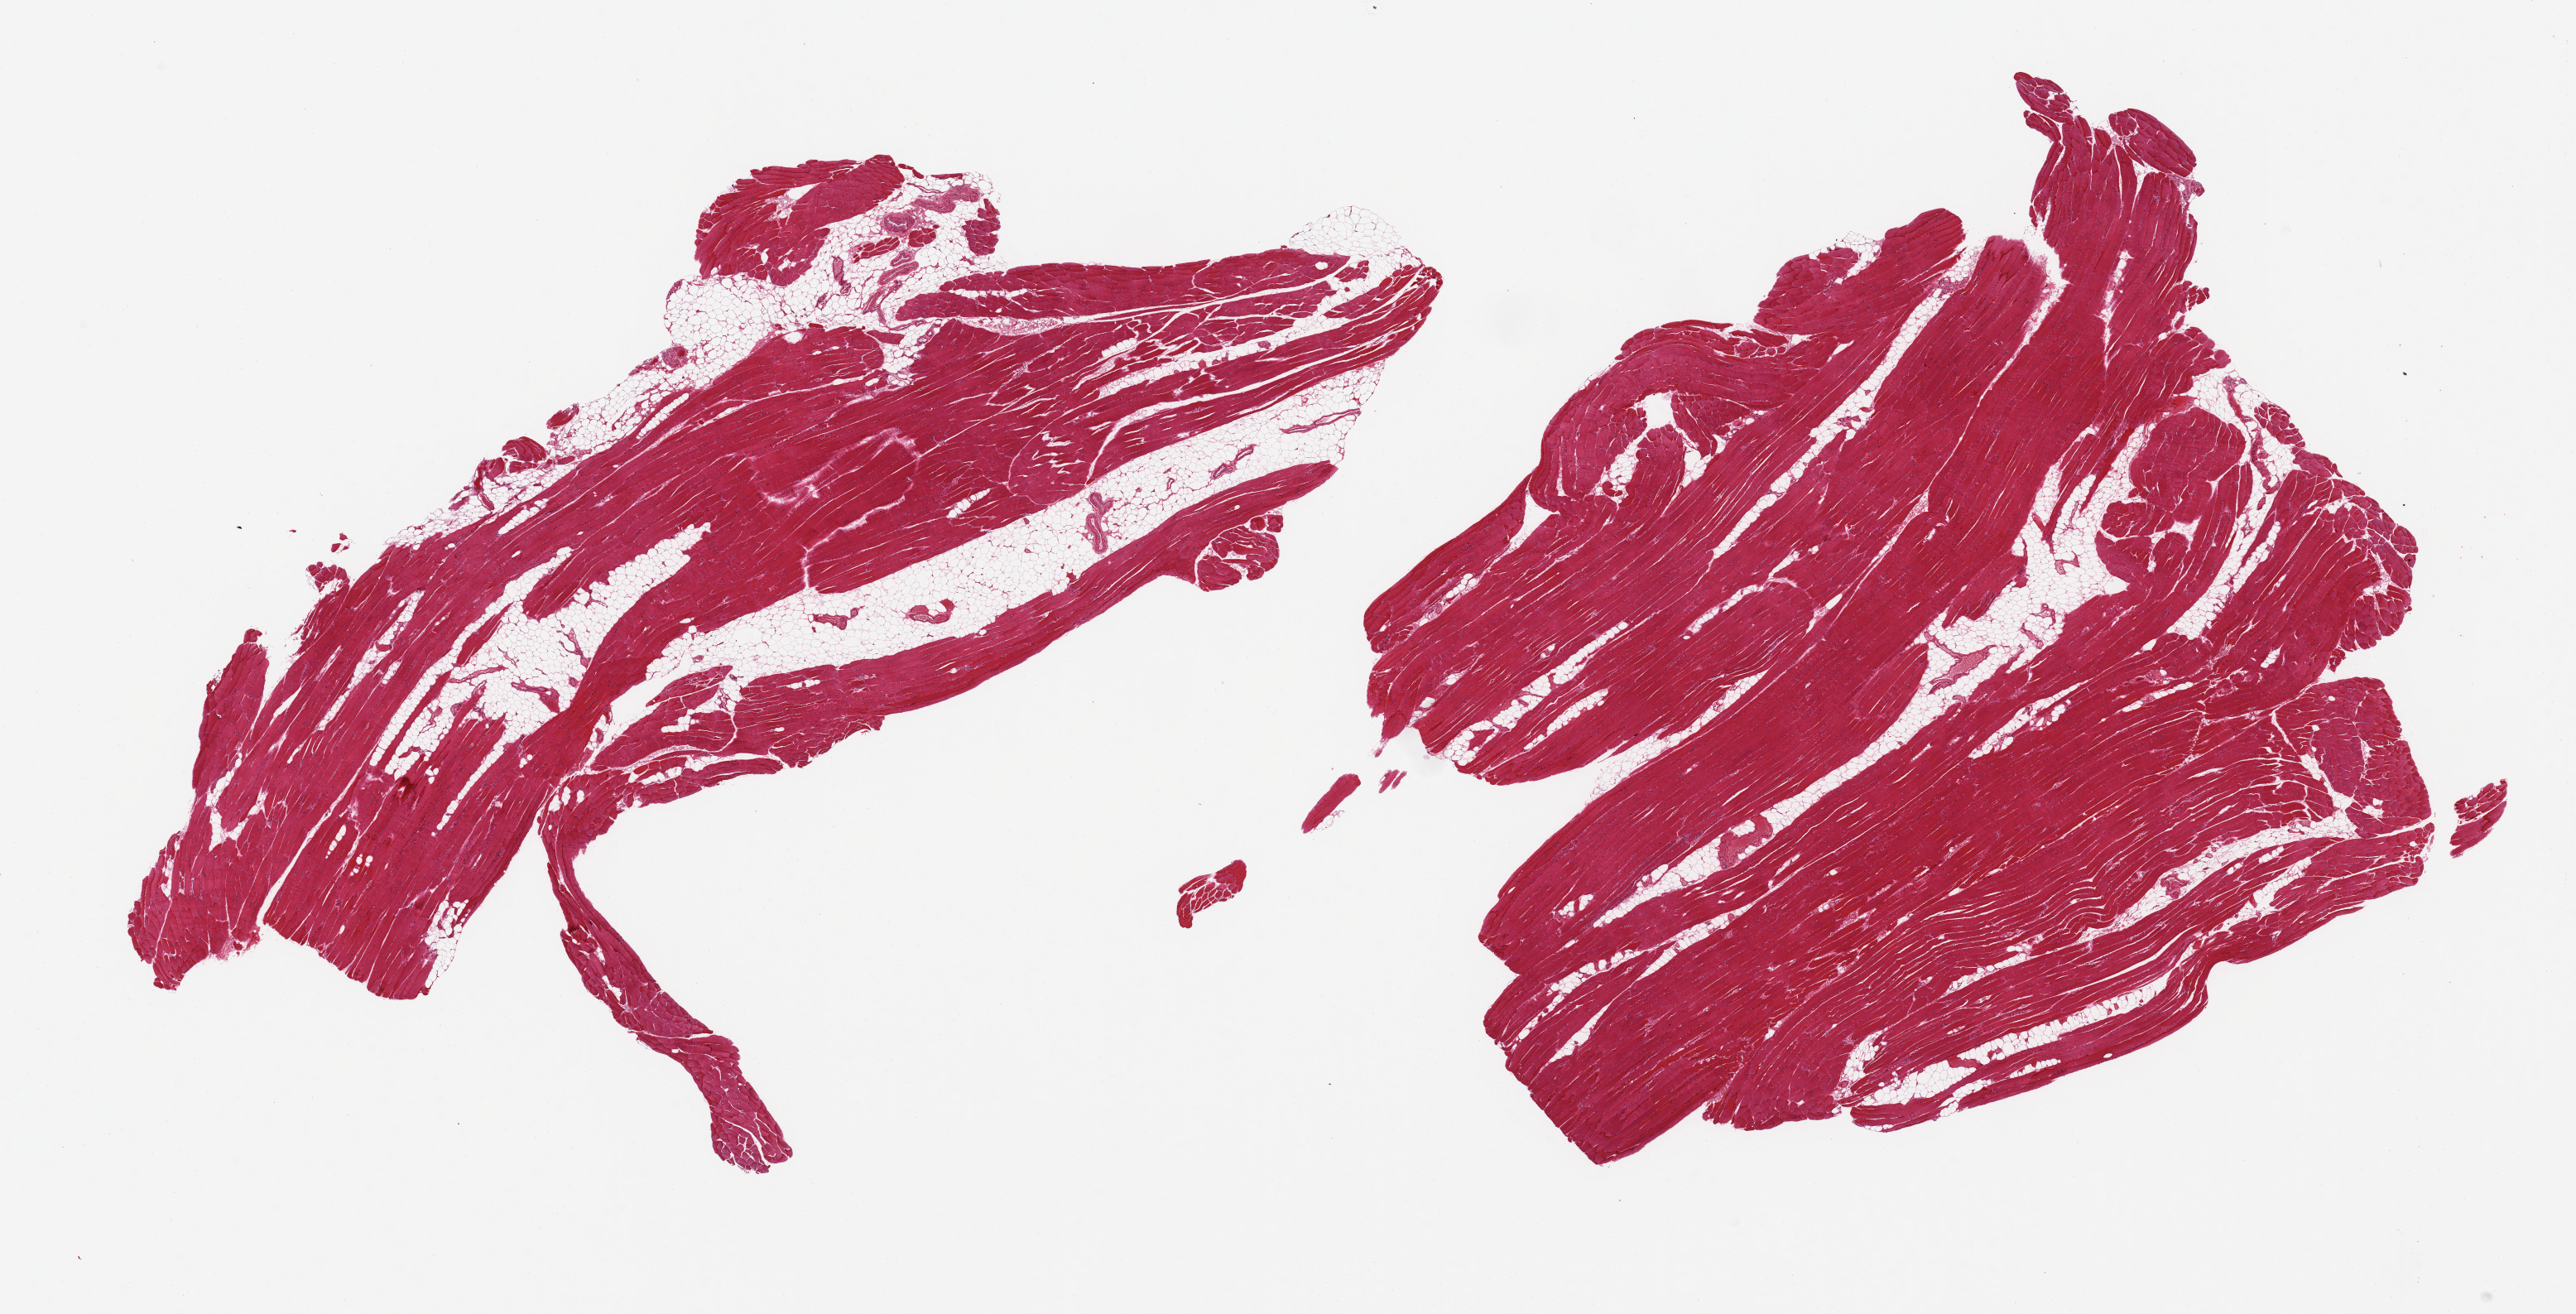
Whole-slide image, hematoxylin and eosin (H&E) stain, brightfield — a low-resolution overview of the entire scanned area, about 24.6 x 12.6 mm (slide scanned at 20x). PAXgene-fixed paraffin-embedded (PFPE) section. Target tissue: skeletal muscle. Tissue donor sample. Donor: male.
- reviewer comment on this tissue sample: 2 pieces; skeletal muscle with from 10-20% mostly internal fat